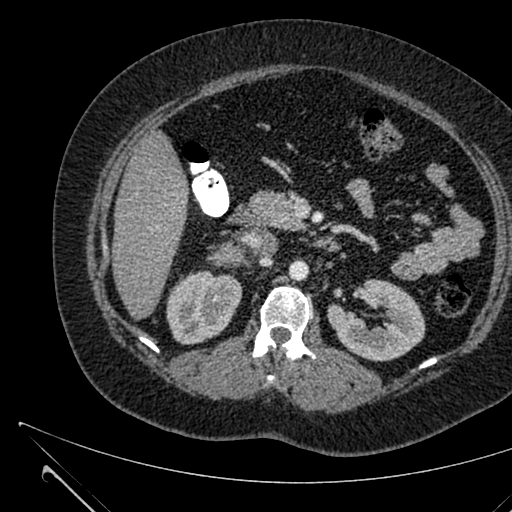
Contrast-enhanced abdominal CT, one axial slice. Position 351 of 731 along the scan axis. 120 kVp. Intravenous contrast given. Soft-tissue window (W 400 / L 40 HU). 1 mm slice thickness. 512 × 512 image matrix. Patient: female, 36 years. Case-level facts recorded for this patient, not image findings: diagnosis: adrenocortical carcinoma; tumour side: right adrenal; tumour size at pathology: 10 cm; Ki-67 index: 20 %; stage (as recorded): 4.
Outlined on this slice (semi-automatic segmentation, software-assisted and operator-edited):
- mass: box from (x=216, y=242) to (x=243, y=264) px